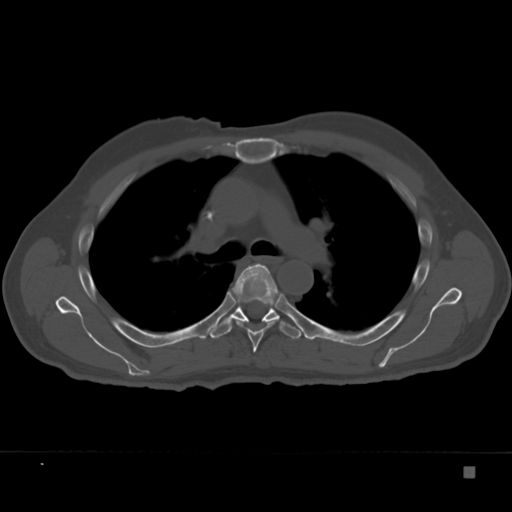
CT including the spine, one axial slice. Slice 249 of 332 in the series (ordered by position). Reconstruction kernel Br40s. 120 kVp. Bone window (W 1800 / L 400 HU). 1.5 mm slice thickness. 512 × 512 image matrix, field of view 389 × 389 mm. Male patient, age 72 years. From the clinical record (not read from this slice): primary cancer: skeletal.
Annotated regions visible in this slice (semi-automatically segmented with operator editing):
- T5 vertebra: box from (x=232, y=263) to (x=281, y=353) px
- T6 vertebra: (x=209, y=296)–(x=302, y=339)